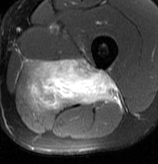
MRI of an extremity soft-tissue mass, one axial slice. Position 45 of 70 along the scan axis. T2-weighted fat-saturated. MR volume resampled by the dataset authors to the PET/CT grid (not the native acquisition matrix). 158 × 164 image matrix, field of view 154 × 160 mm. Male patient. From the clinical record (not read from this slice): histological type: extraskeletal osteosarcoma; grade: high; site of the primary tumour: left adductur.
Structures marked on this image (expert contour drawn on MRI and transferred to this co-registered scan by the dataset authors):
- gross tumour volume (mass): bounding box (x1, y1, x2, y2) in pixels: (24, 57, 121, 111)